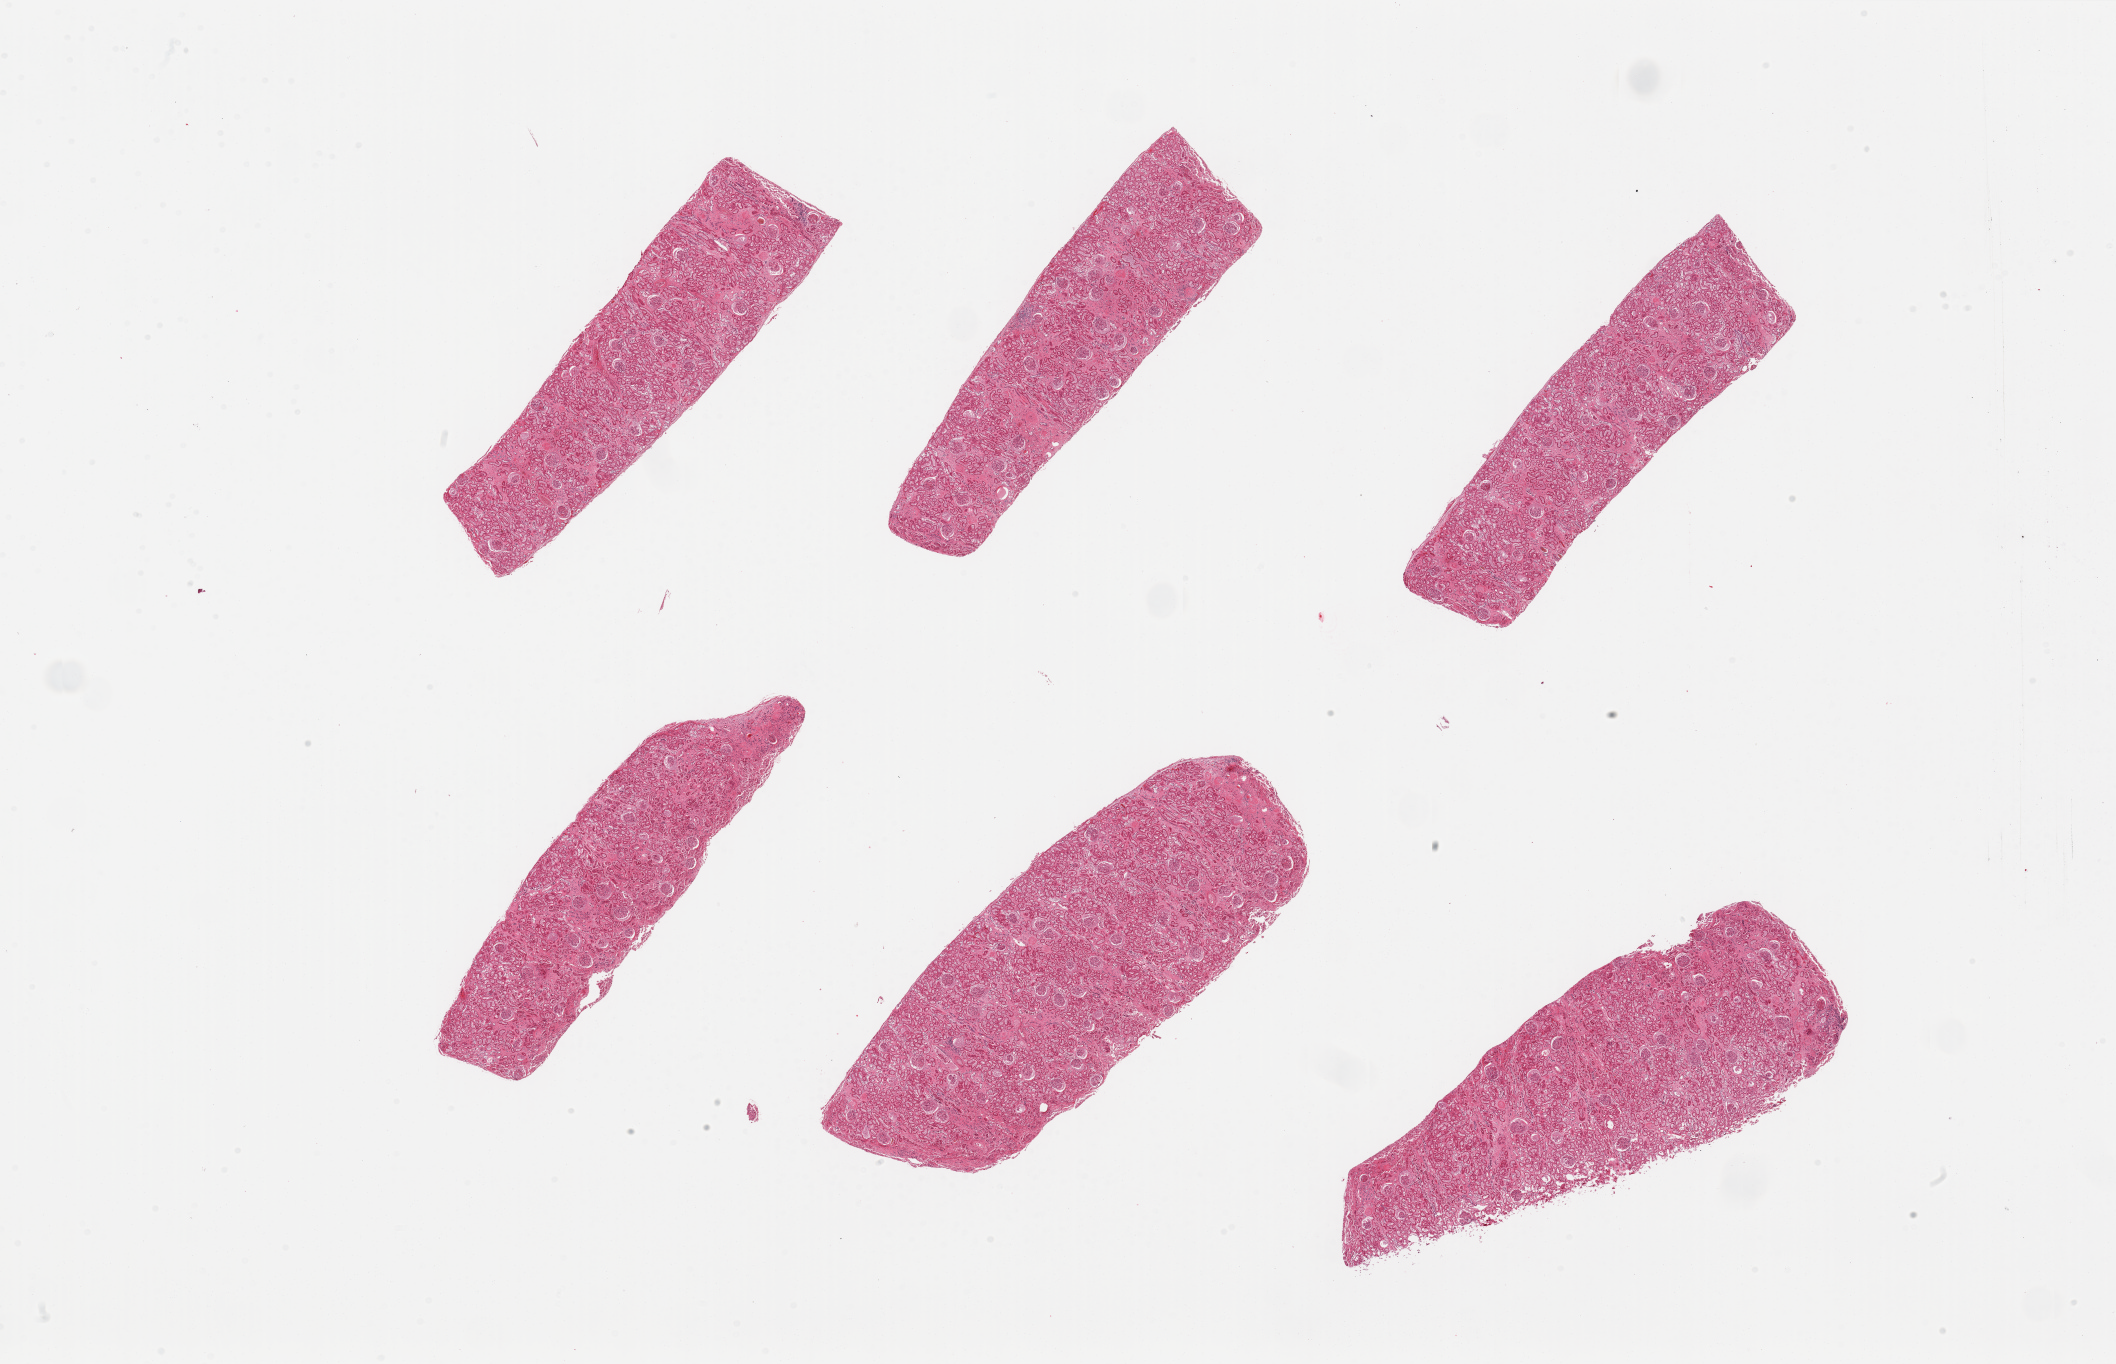
H&E whole-slide image, low-resolution overview of the scanned area, about 33.5 x 21.6 mm; PAXgene-fixed, paraffin-embedded tissue; section of renal cortex (target tissue); tissue donor sample. Male donor.
Review note (as recorded): 6 pieces, all contain glomeruli, tubules badly autolyzed.